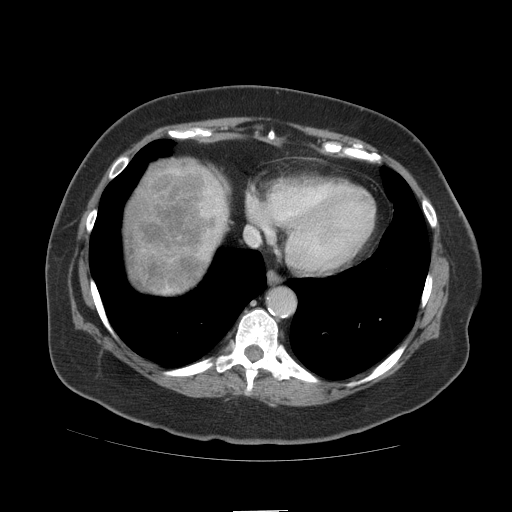
Contrast-enhanced abdominal CT (liver protocol), one axial slice. Slice 98 of 109 in the series (ordered by position). Reconstruction kernel STANDARD. Soft-tissue window (W 400 / L 40 HU). 2.5 mm slice thickness. 512 × 512 image matrix, field of view 420 × 420 mm. From the clinical record (not read from this slice): diagnosis: hepatocellular carcinoma (patient treated with transarterial chemoembolisation; whether this scan precedes or follows treatment is not stated here); TNM stage (as recorded): Stage-IVB; Child-Pugh class: A; tumour differentiation: poorly differentiated; tumour nodularity: multinodular.
Structures marked on this image (semi-automatically segmented with operator editing):
- liver parenchyma outside the tumour (the mass and vessels are separate outlines, so this box may not span the whole liver): bounding box <128,158,228,294> (left, top, right, bottom; pixels)
- mass: <125,163,225,289>